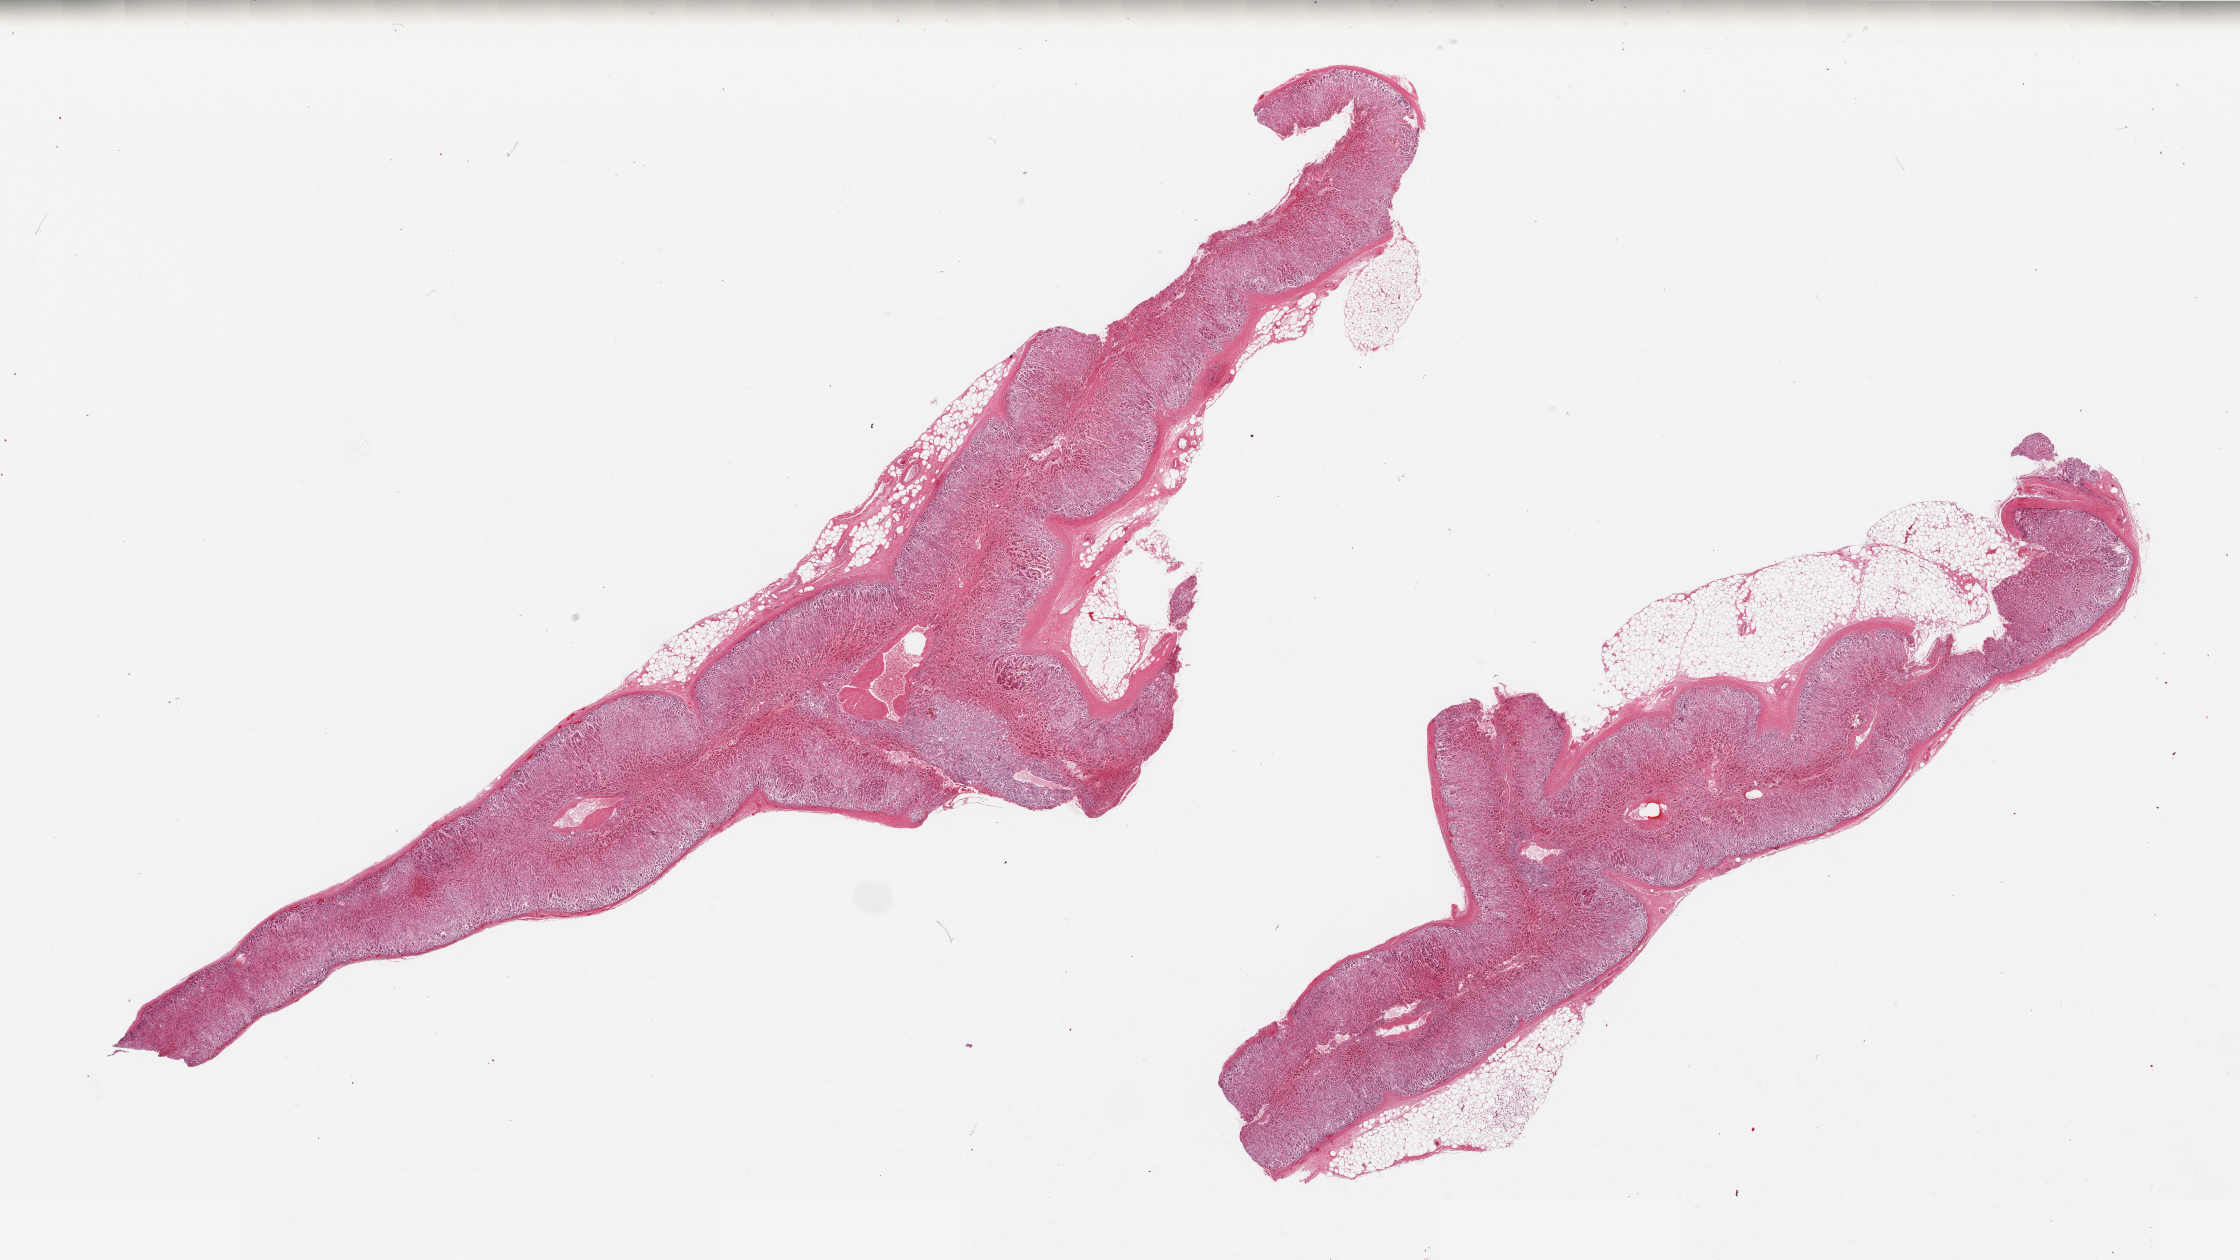
Whole-slide image, haematoxylin and eosin stain, brightfield, whole scanned area (about 35.4 x 19.9 mm, acquisition: 20x scan) shown as a low-resolution overview, PAXgene-fixed paraffin-embedded (PFPE) section, target tissue: adrenal gland, tissue donor sample. Donor: male.
* review note (as recorded): 2 pieces, 10-15% attached fat